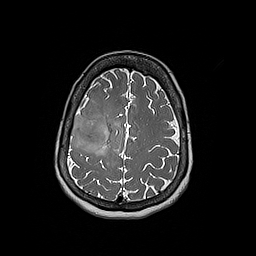
Brain MRI from a brain-tumour surgery series, one axial slice. Slice 60 of 192 in the series (ordered by position). 256 × 256 image matrix. Case-level facts recorded for this patient, not image findings: histopathology: Oligodendroglioma; WHO grade: 3; IDH mutation: yes; tumour location: Right Frontal.
Outlined on this slice (expert manual segmentation):
- tumour: bounding box <70,114,107,153> (left, top, right, bottom; pixels)